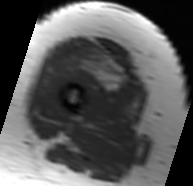
MRI of an extremity soft-tissue mass, one axial slice; position 22 of 91 along the scan axis; MR volume resampled by the dataset authors to the PET/CT grid (not the native acquisition matrix); 3.27 mm slice thickness; 193 × 186 image matrix, field of view 188 × 182 mm. Female patient. Case-level facts recorded for this patient, not image findings: histological type: malignant solitary fibrous tumor; grade: intermediate; site of the primary tumour: right thigh.
Structures marked on this image (expert contour drawn on MRI and transferred to this co-registered scan by the dataset authors):
- gross tumour volume including surrounding oedema: bounding box <60,37,141,100> (left, top, right, bottom; pixels)